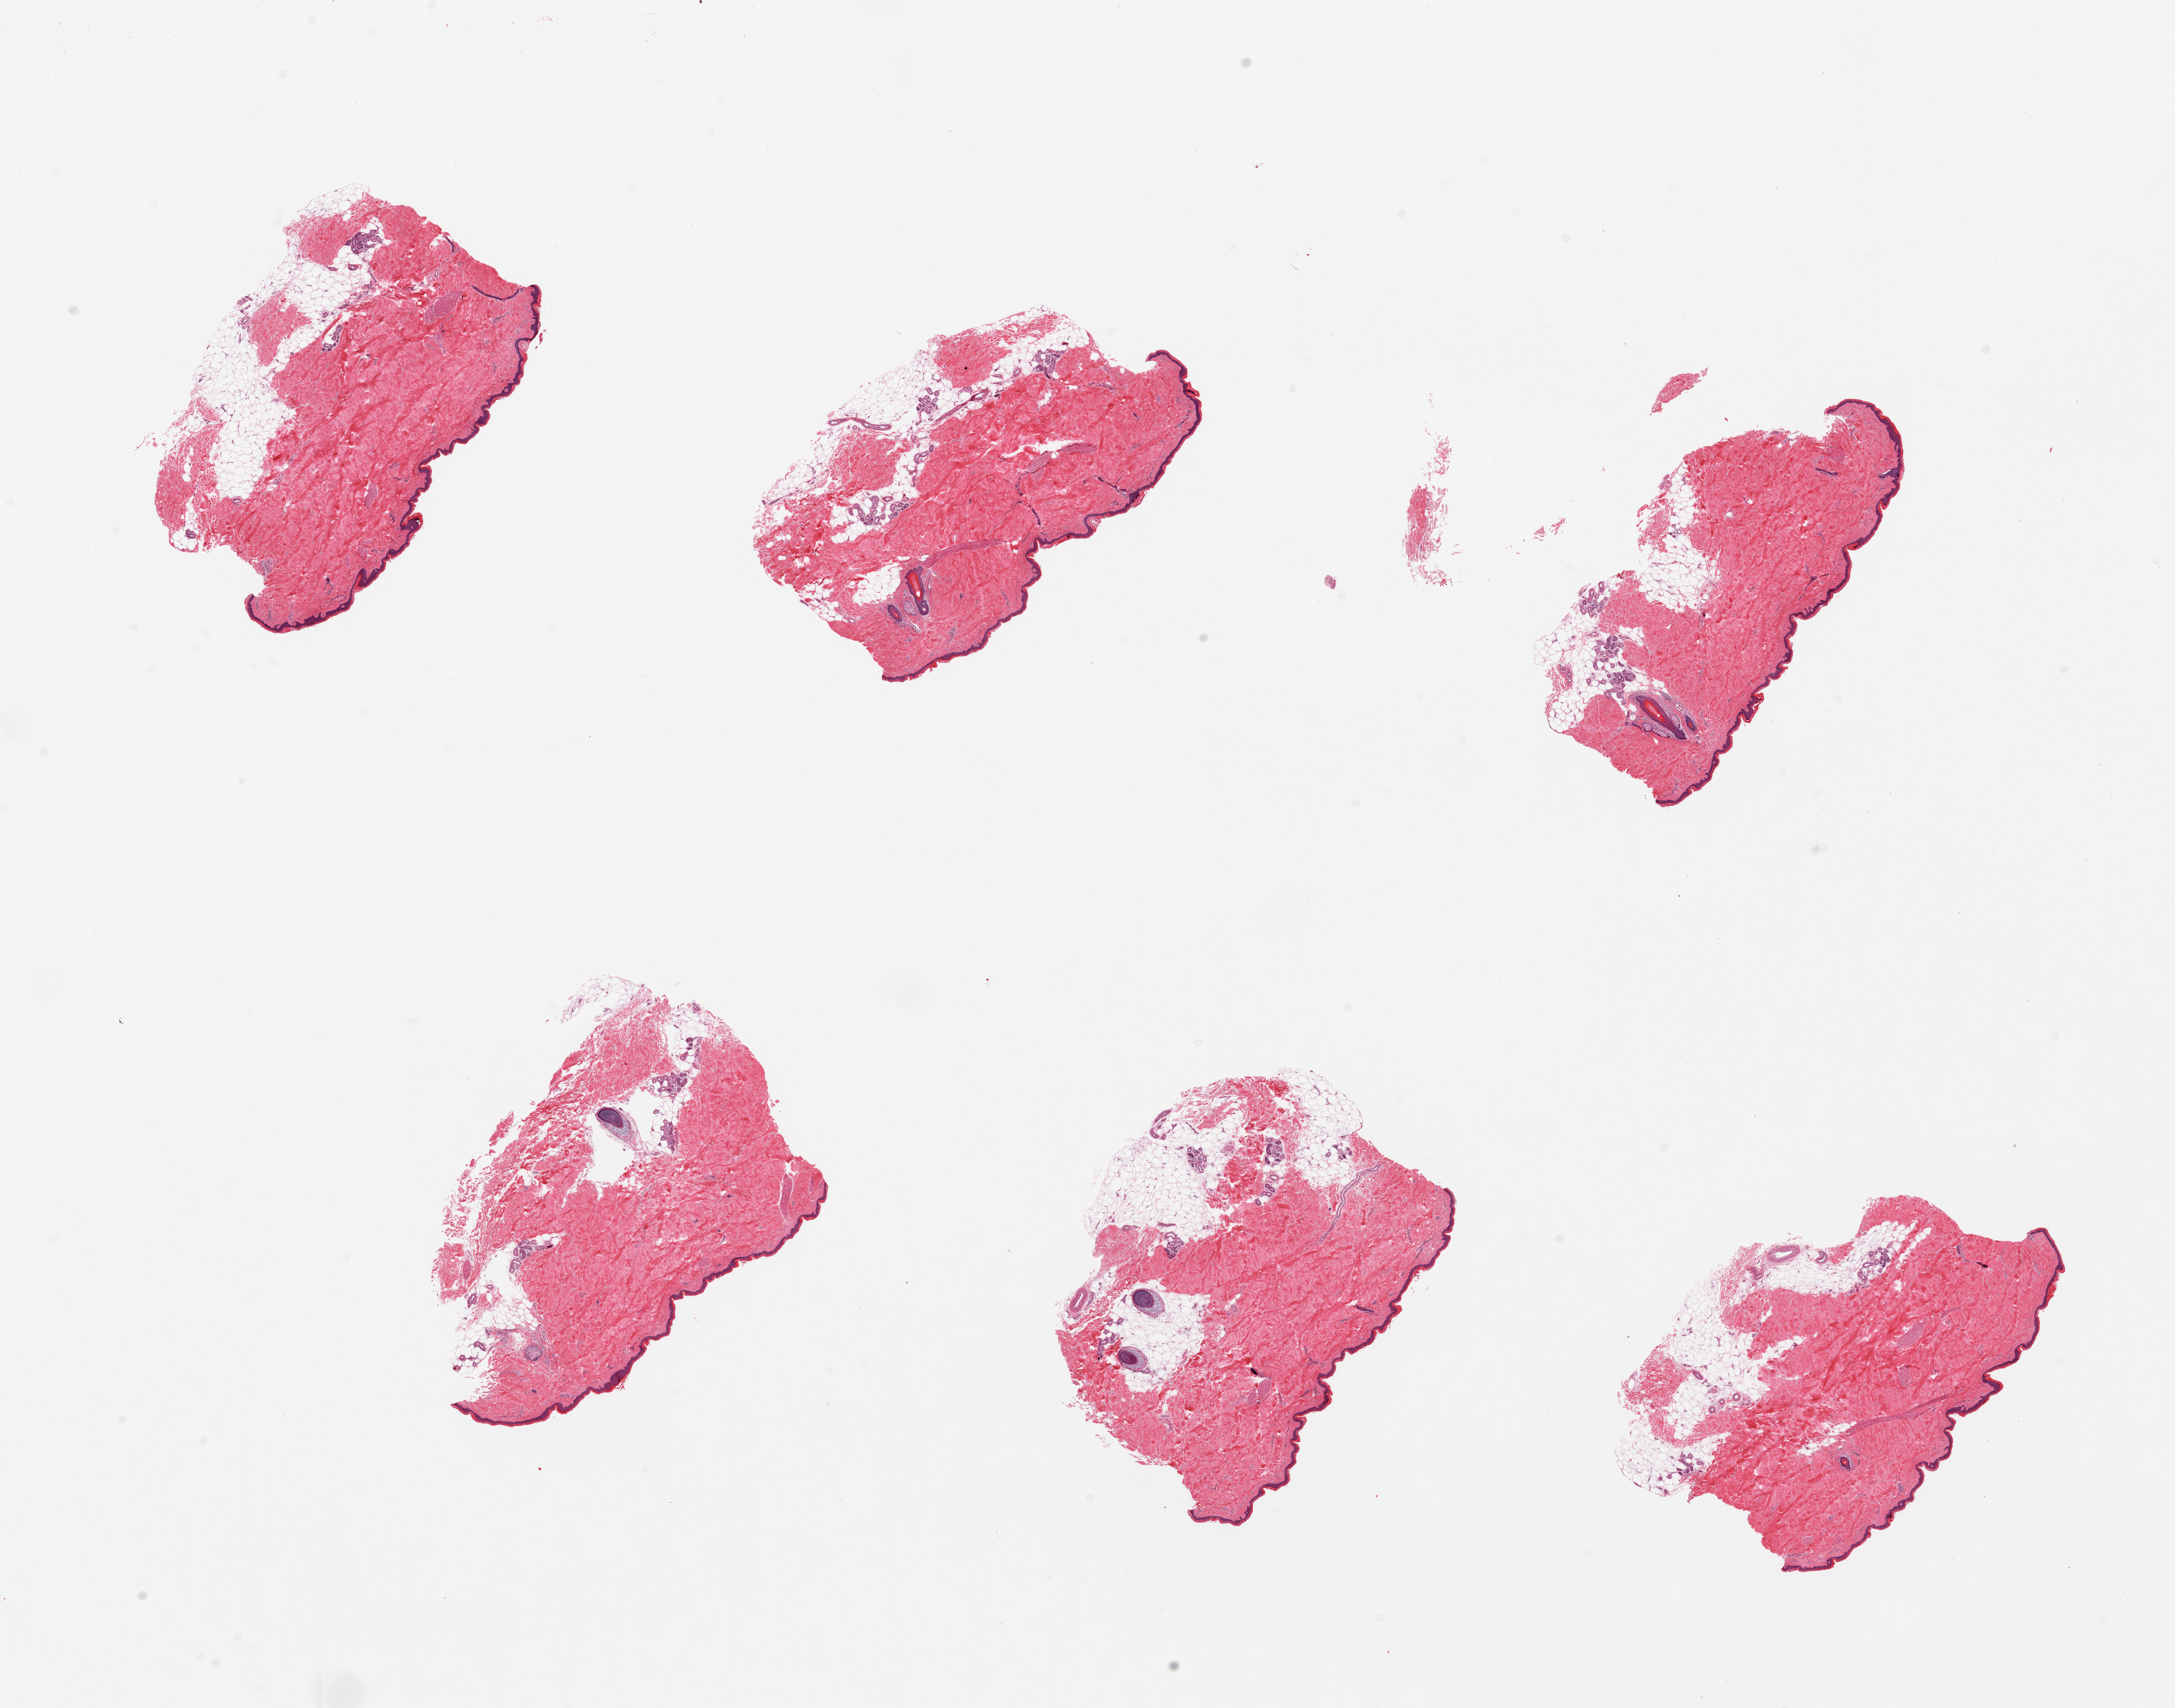
Whole-slide image, H&E stain, whole scanned area (about 26.6 x 20.9 mm, slide scanned at 20x) shown as a low-resolution overview, PAXgene-fixed, paraffin-embedded tissue, sampled site (target tissue): skin of lower leg, donor tissue sample. Donor: male.
• reviewer comment on this tissue sample: 6 pieces, trace adherent dermal fat; squamous epithelium is ~45microns thick